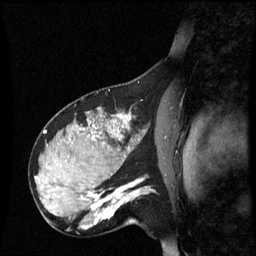
Breast MRI (dynamic contrast-enhanced), one sagittal slice. Position 38 of 60 along the scan axis. Dynamic contrast-enhanced series, image 2 of 3 at this slice position (ordered by acquisition). 1.5 T. TE 4.2 ms, TR 8.9 ms. 256 × 256 image matrix, field of view 220 × 220 mm. Female patient, age 31 years. From the clinical record (not read from this slice): setting: breast cancer imaged before/during neoadjuvant chemotherapy; receptor status: HR-positive, HER2-negative.
Annotated regions visible in this slice (semi-automatic segmentation, software-assisted and operator-edited):
- analysis volume of interest (the breast-tissue region the enhancement analysis was run in; not a lesion): box from (x=90, y=180) to (x=151, y=227) px
- tumour enhancement mask (voxels above the 70 % enhancement threshold inside the analysis volume of interest): (x=91, y=180)–(x=142, y=225)